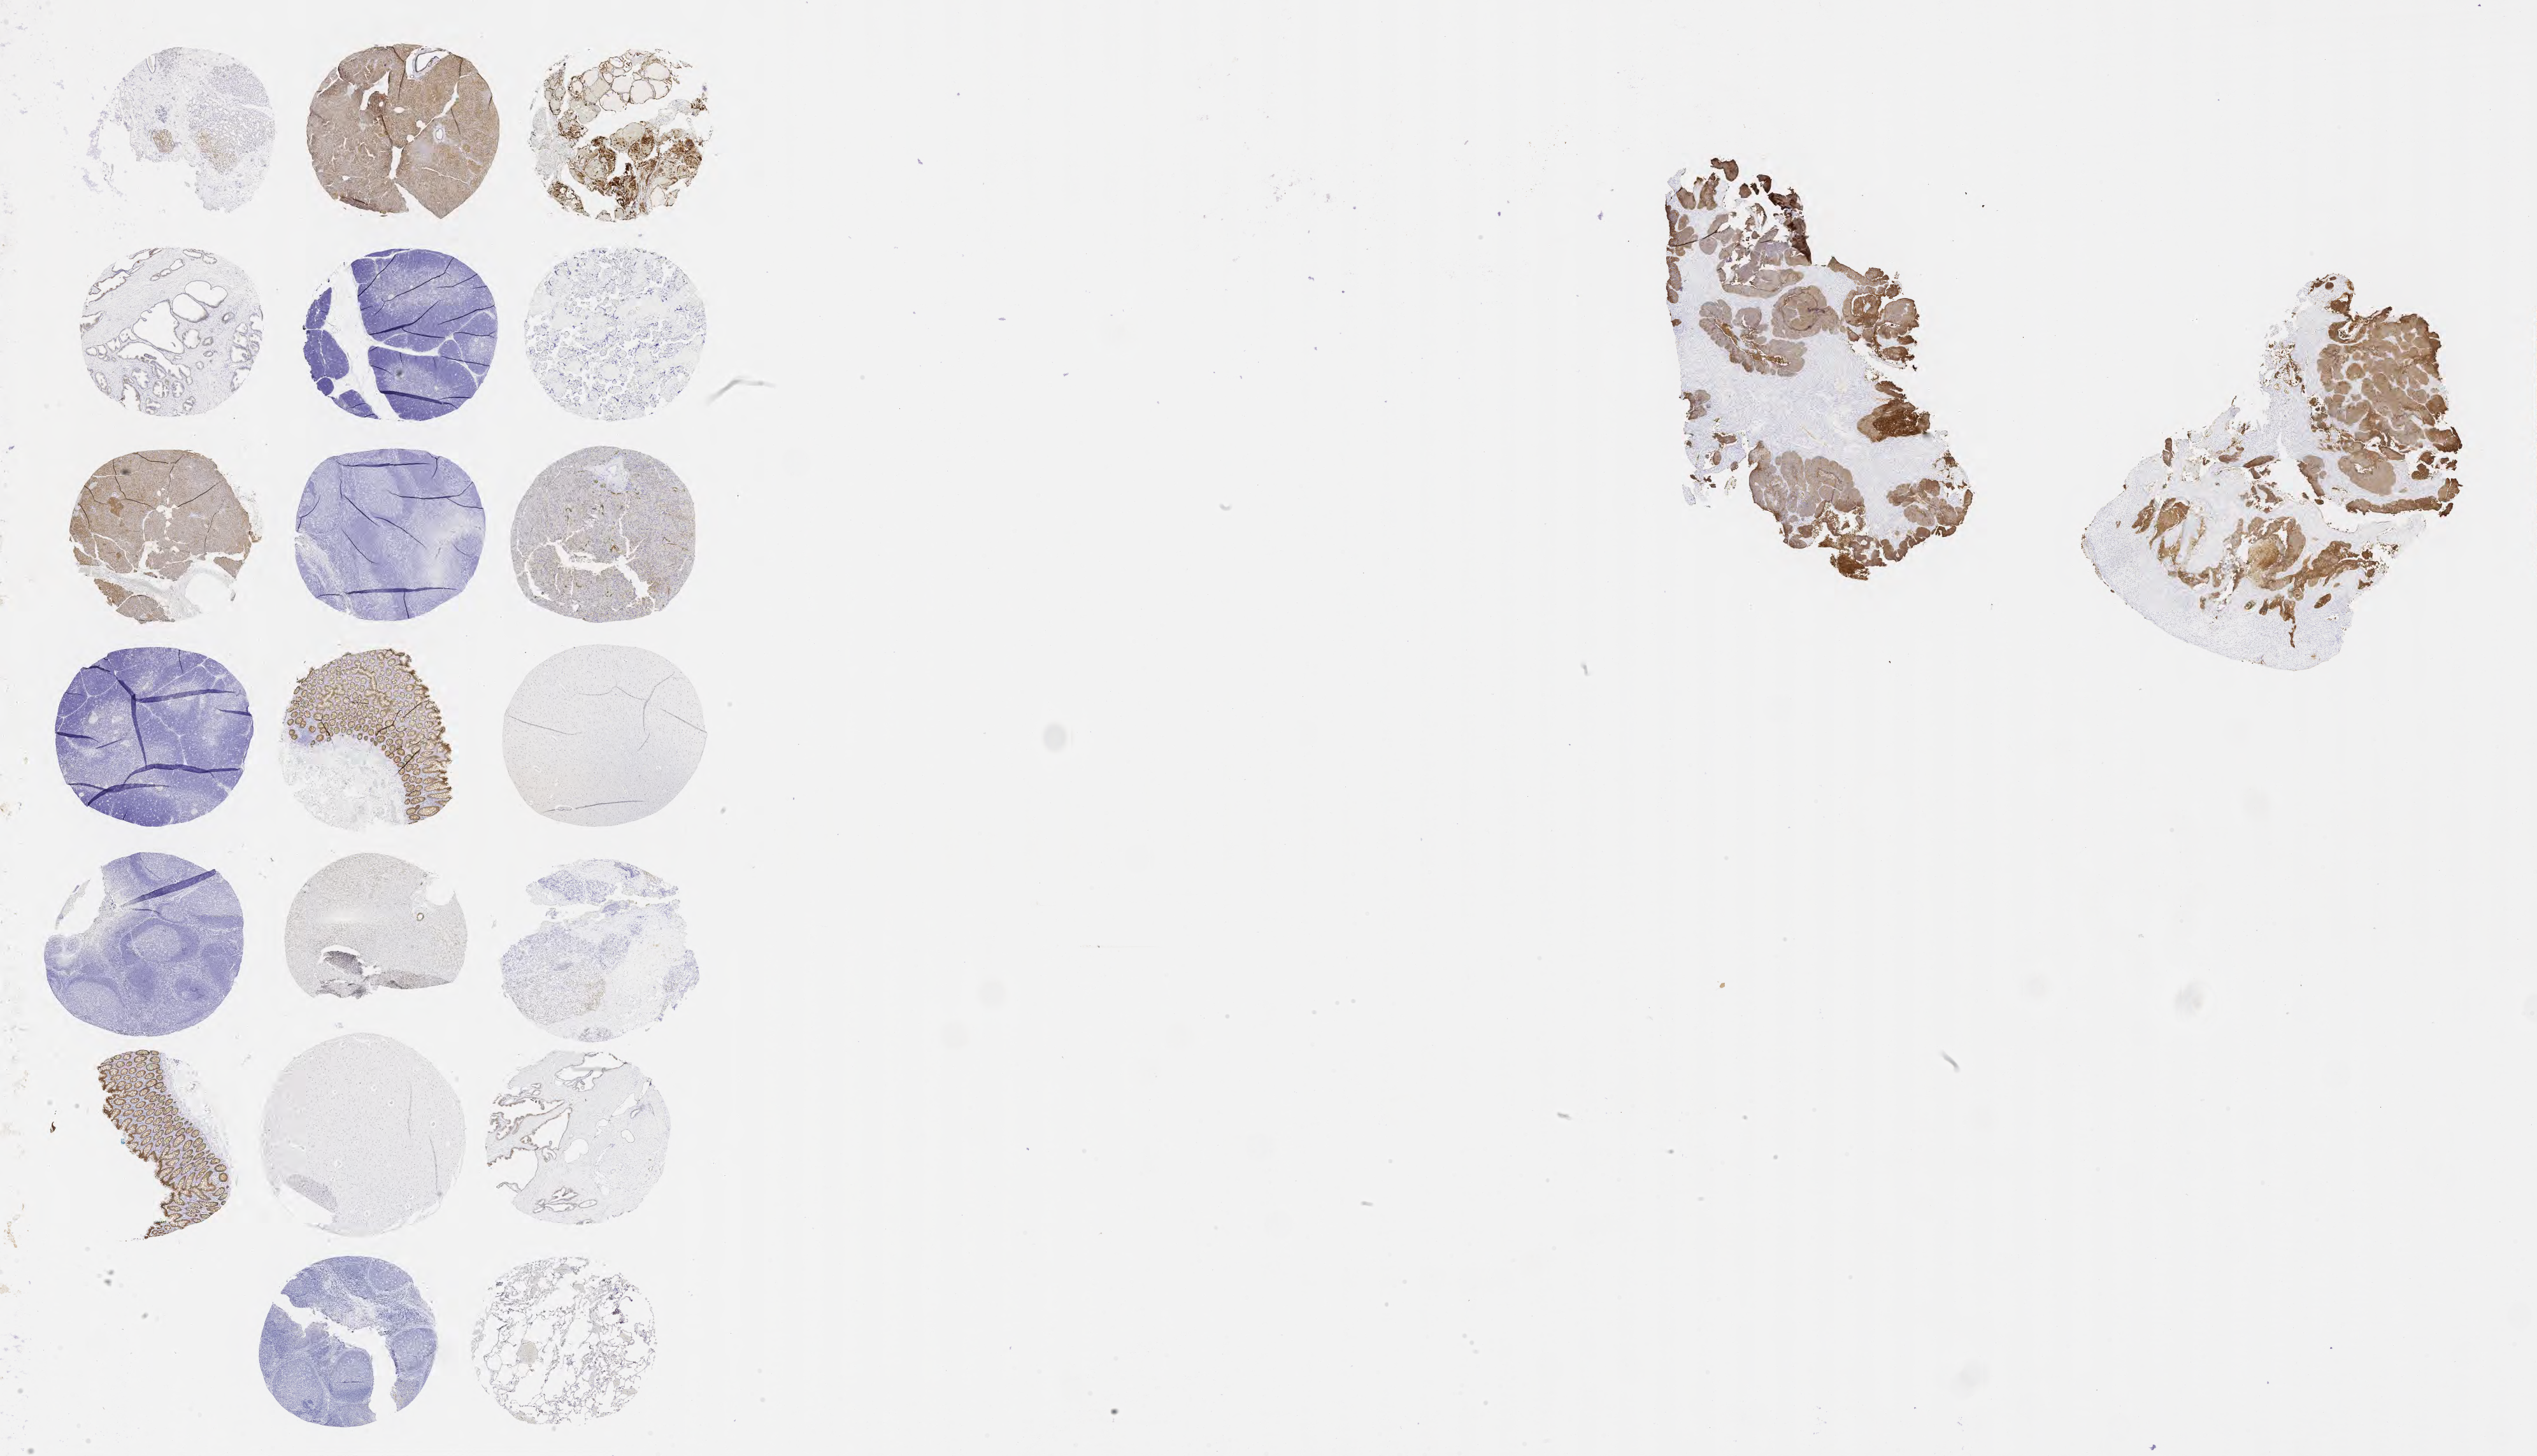
Whole-slide image, immunohistochemical stain for MOC-31 (anti-EpCAM) — shown as a low-resolution overview of the whole scanned area (about 32.2 x 18.5 mm); specimen: tumor tissue; site: cervix. Patient female; aged 38.
Diagnosis: Squamous cell carcinoma, large cell, nonkeratinizing, NOS.